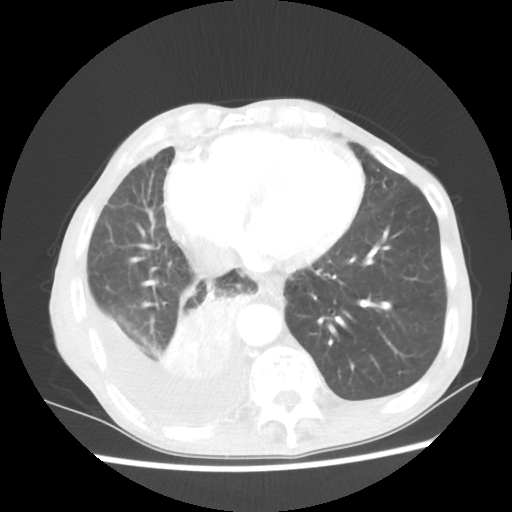
Chest CT, one axial slice. Slice 19 of 60 in the series (ordered by position). Reconstruction kernel STANDARD. 80 kVp. Lung window (W 1500 / L -600 HU). 5 mm slice thickness. 512 × 512 image matrix, field of view 335 × 335 mm. Male patient, age 76 years. From the clinical record (not read from this slice): clinical TNM (as recorded): T3 N3 M1a; histopathological grade: G3.
Structures marked on this image (rectangle marked by the reading radiologist):
- lung tumour (recorded histology: squamous cell carcinoma): box from (x=155, y=283) to (x=251, y=382) px